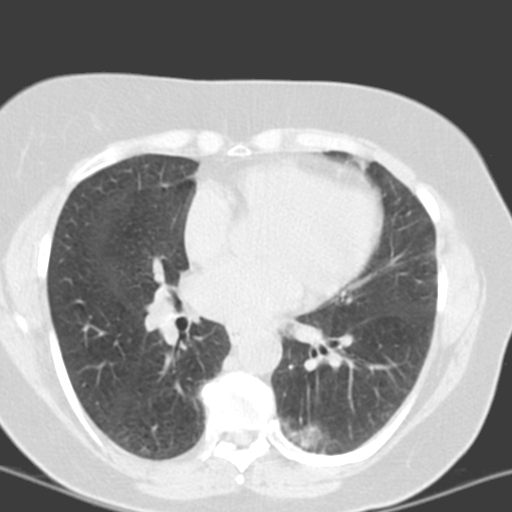
Low-dose screening chest CT, axial slice. Third screening round (two years after baseline). Lung window (W 1500 / L -600 HU). 3.2 mm slice thickness. Standard (soft-tissue) reconstruction kernel (B). 120 kVp. Slice 73 of 150 in the series. 512 × 512 image matrix. Female participant, aged 55 years at enrolment. Current smoker at enrolment.
Lesion marked by an expert reader, bounding box <276,403,358,460> (left, top, right, bottom; pixels). The screening reader recorded 6 non-calcified nodules or masses ≥4 mm on this exam (left lower lobe, left lower lobe, left upper lobe, lingula, lingula, right middle lobe); which of them this box marks is not recorded. Official screen result: positive, no significant change: stable abnormalities potentially related to lung cancer, unchanged since the prior screening exam.